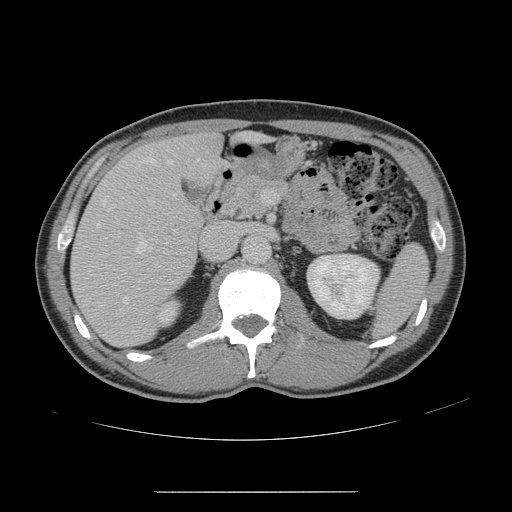
Contrast-enhanced abdominal CT, one axial slice; position 80 of 178 along the scan axis; 120 kVp; intravenous contrast given; soft-tissue window (W 400 / L 40 HU); 512 × 512 image matrix. Male patient, age 53 years. Case-level facts recorded for this patient, not image findings: diagnosis: colorectal cancer liver metastases, imaged before liver resection; multiple liver metastases: yes.
Annotated regions visible in this slice (manually delineated by an expert):
- hepatic veins: bounding box [x1, y1, x2, y2] px = [96, 158, 199, 305]
- liver: [71, 134, 222, 347]
- planned liver remnant (the part of the liver to remain after resection): [161, 134, 221, 177]
- portal vein (with intrahepatic branches): [148, 191, 267, 268]